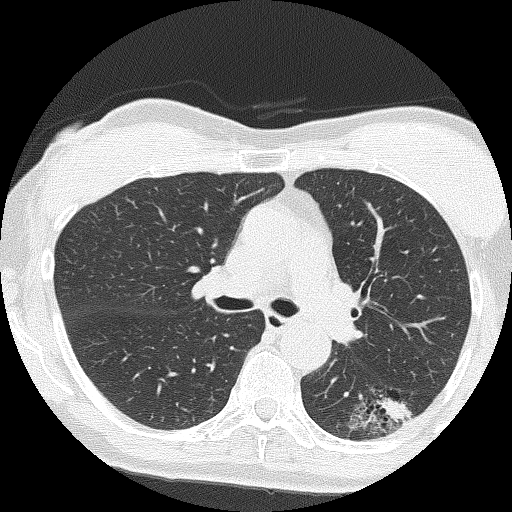
Chest CT (low-dose screening protocol), one axial image; second screening round (one year after baseline); lung window (W 1500 / L -600 HU); lung (sharp) reconstruction kernel (FC51); 120 kVp; slice 61 of 159 in the series; 512 × 512 image matrix. Female participant, aged 64 years at enrolment. Former smoker at enrolment.
• Lesion marked by an expert reader, bounding box [x1, y1, x2, y2] px = [356, 380, 428, 439].
• The screening reader recorded 3 non-calcified nodules or masses ≥4 mm on this exam (right upper lobe, right upper lobe, right middle lobe); which of them this box marks is not recorded.
• Lung cancer was diagnosed 576 days after this screen: adenocarcinoma, NOS, left lower lobe, moderately differentiated (G2), stage IA (AJCC 6th edition), 17 mm at pathology.